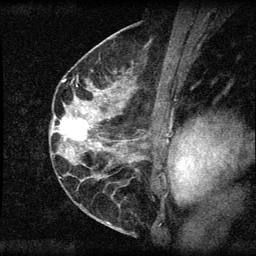
Breast MRI (dynamic contrast-enhanced), one sagittal slice; slice 33 of 60 in the series (ordered by position); dynamic contrast-enhanced series, image 2 of 3 at this slice position (ordered by acquisition); 1.5 T; TE 4.2 ms, TR 8.2 ms; 2 mm slice thickness; 256 × 256 image matrix, field of view 180 × 180 mm. Patient: female, 45 years.
Annotated regions visible in this slice (semi-automatic segmentation, software-assisted and operator-edited):
- analysis volume of interest (the breast-tissue region the enhancement analysis was run in; not a lesion): bounding box [x1, y1, x2, y2] px = [55, 110, 94, 148]
- tumour enhancement mask (voxels above the 70 % enhancement threshold inside the analysis volume of interest): [55, 117, 88, 141]